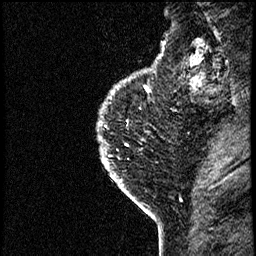
Breast MRI (dynamic contrast-enhanced), one sagittal slice. Slice 56 of 60 in the series (ordered by position). Dynamic contrast-enhanced study with each time point stored as its own series, time point 2 of 4 at this slice position (early post-contrast, ordered by acquisition time). 1.5 T. TE 4.2 ms, TR 17.6 ms. 256 × 256 image matrix. Female patient, age 40 years. Case-level facts recorded for this patient, not image findings: setting: breast cancer imaged before/during neoadjuvant chemotherapy; receptor status: HER2-positive.
Structures marked on this image (semi-automatic segmentation, software-assisted and operator-edited):
- analysis volume of interest (the breast-tissue region the enhancement analysis was run in; not a lesion): bounding box (x1, y1, x2, y2) in pixels: (91, 55, 185, 206)
- tumour enhancement mask (voxels above the 100 % enhancement threshold inside the analysis volume of interest): (102, 55, 162, 206)